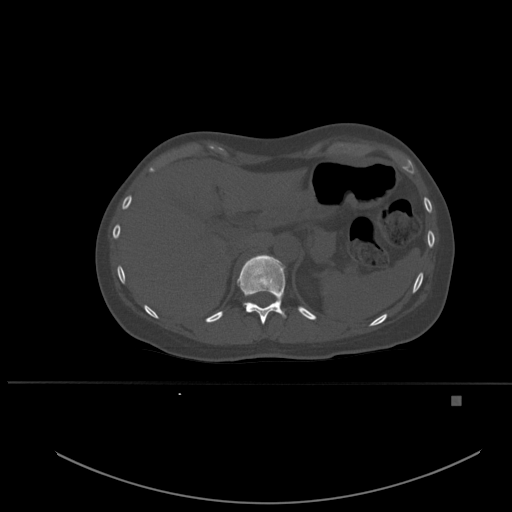
CT including the spine, one axial slice. Position 270 of 651 along the scan axis. Bone window (W 1800 / L 400 HU). 1.5 mm slice thickness. 512 × 512 image matrix, field of view 443 × 443 mm. Patient: female, 49 years. Case-level facts recorded for this patient, not image findings: primary cancer: breast.
Structures marked on this image (semi-automatic segmentation, software-assisted and operator-edited):
- T11 vertebra: bounding box (x1, y1, x2, y2) in pixels: (237, 254, 286, 324)